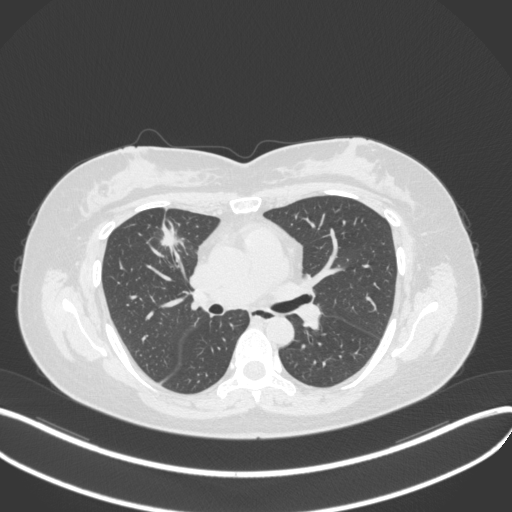
Chest CT, one axial slice. Position 186 of 272 along the scan axis. 120 kVp. Lung window (W 1500 / L -600 HU). 1 mm slice thickness. 512 × 512 image matrix. Female patient, age 42 years. Case-level facts recorded for this patient, not image findings: clinical TNM (as recorded): T1b N0 M0.
Annotated regions visible in this slice (rectangle marked by the reading radiologist):
- lung tumour (recorded histology: adenocarcinoma): box from (x=151, y=208) to (x=187, y=253) px